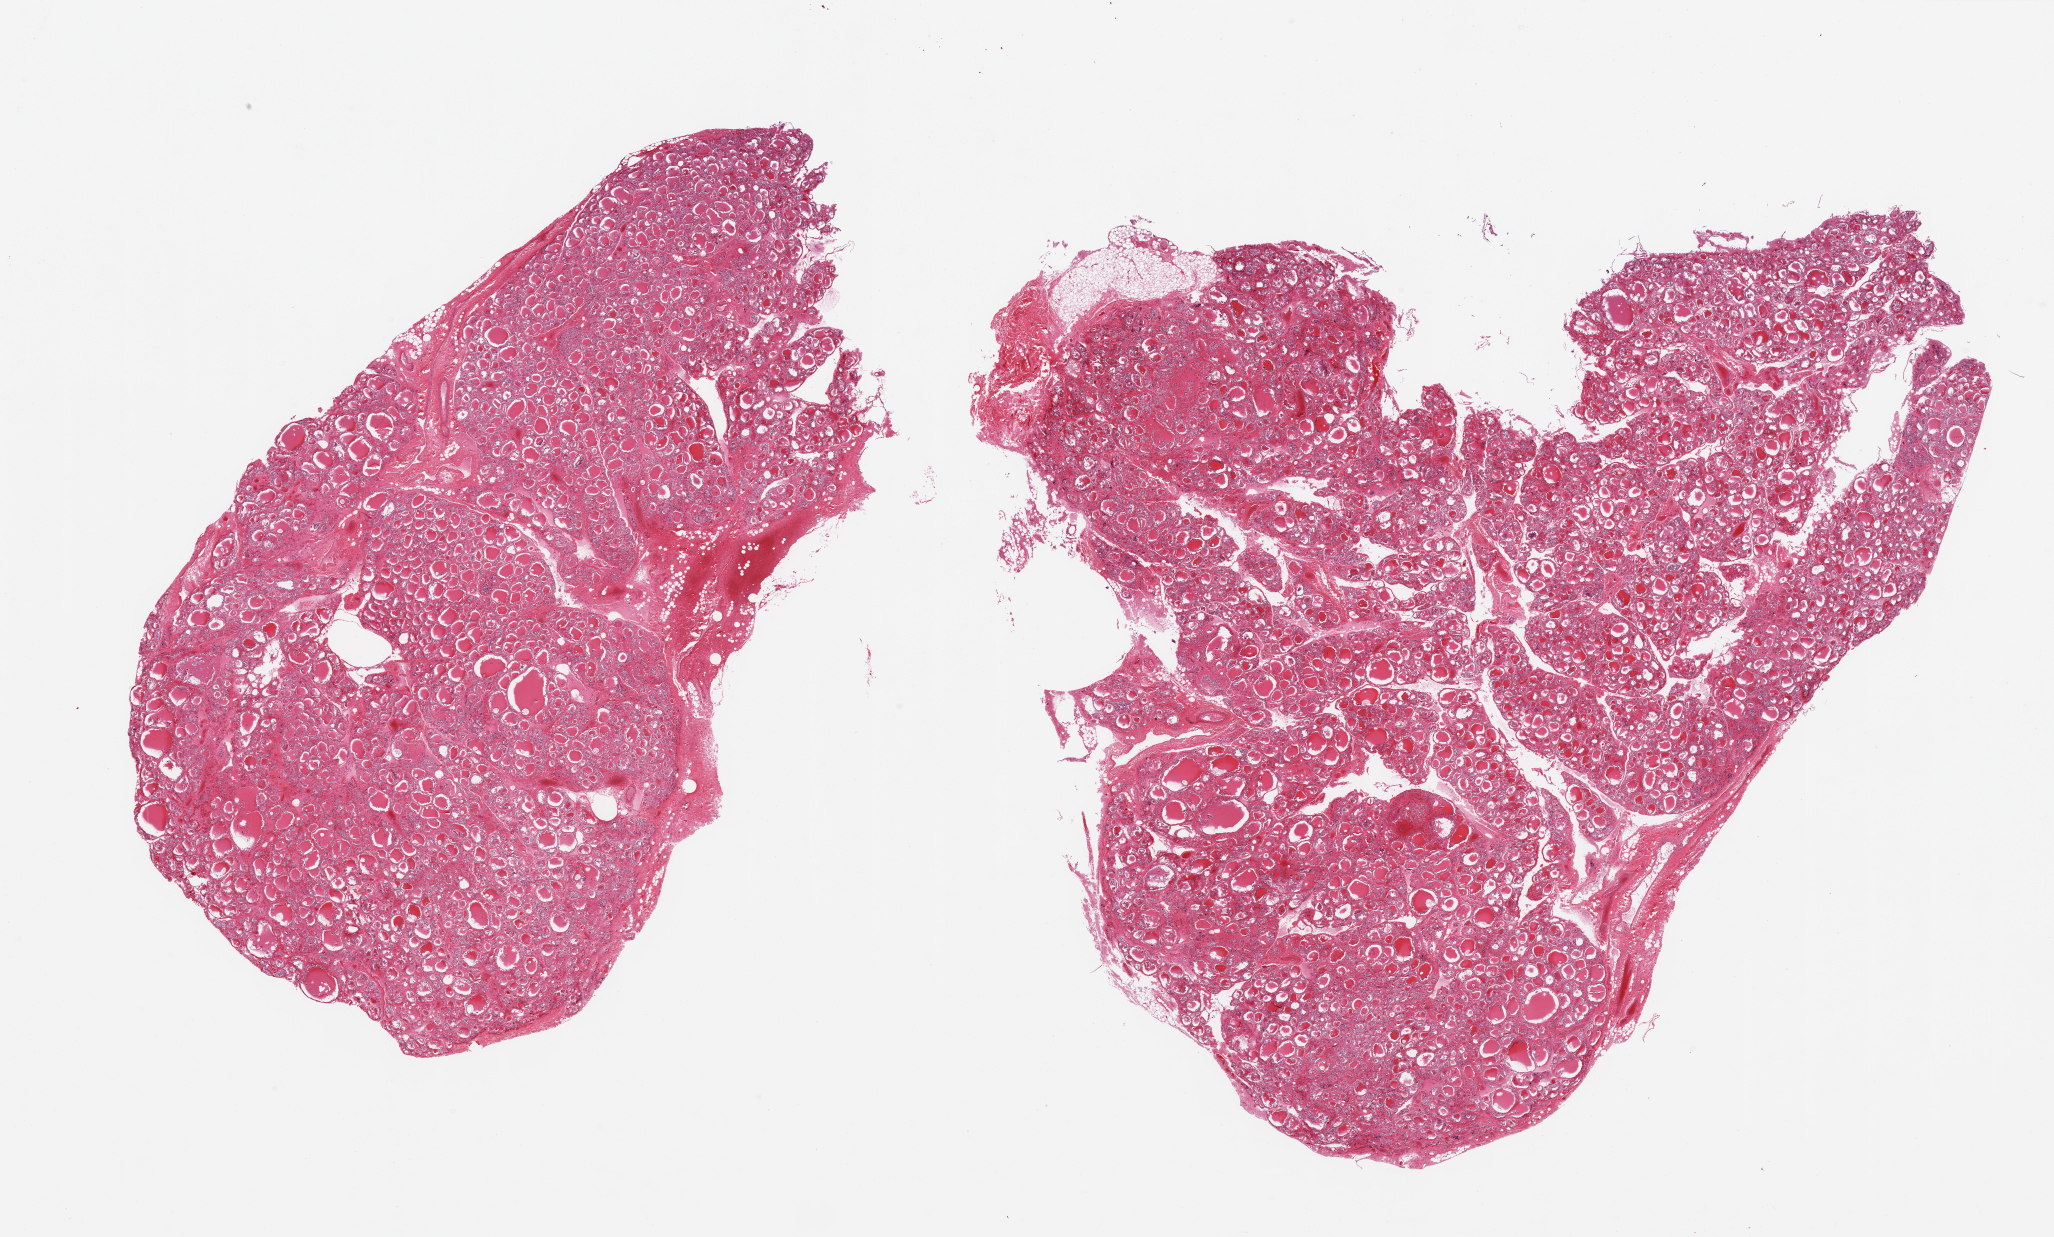
Digitized hematoxylin and eosin (H&E)-stained section — whole scanned area (about 32.5 x 19.6 mm, slide scanned at 20x) shown as a low-resolution overview, PAXgene-fixed, paraffin-embedded tissue, target tissue: thyroid, donor tissue sample. Donor: male.
Pathologist's review note for this sample: 2 pieces, feature of goitre; trace nubbins of fat/fibrous tissue up to ~1mm.